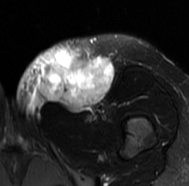
MRI of an extremity soft-tissue mass, one axial slice; slice 32 of 77 in the series (ordered by position); T2-weighted fat-saturated; MR volume resampled by the dataset authors to the PET/CT grid (not the native acquisition matrix); 3.27 mm slice thickness; 189 × 186 image matrix. Female patient. From the clinical record (not read from this slice): histological type: leiomyosarcoma; grade: high; site of the primary tumour: groin.
Outlined on this slice (expert contour drawn on MRI and transferred to this co-registered scan by the dataset authors):
- gross tumour volume including surrounding oedema: bounding box (x1, y1, x2, y2) in pixels: (15, 40, 114, 119)
- gross tumour volume (mass): (38, 52, 114, 110)